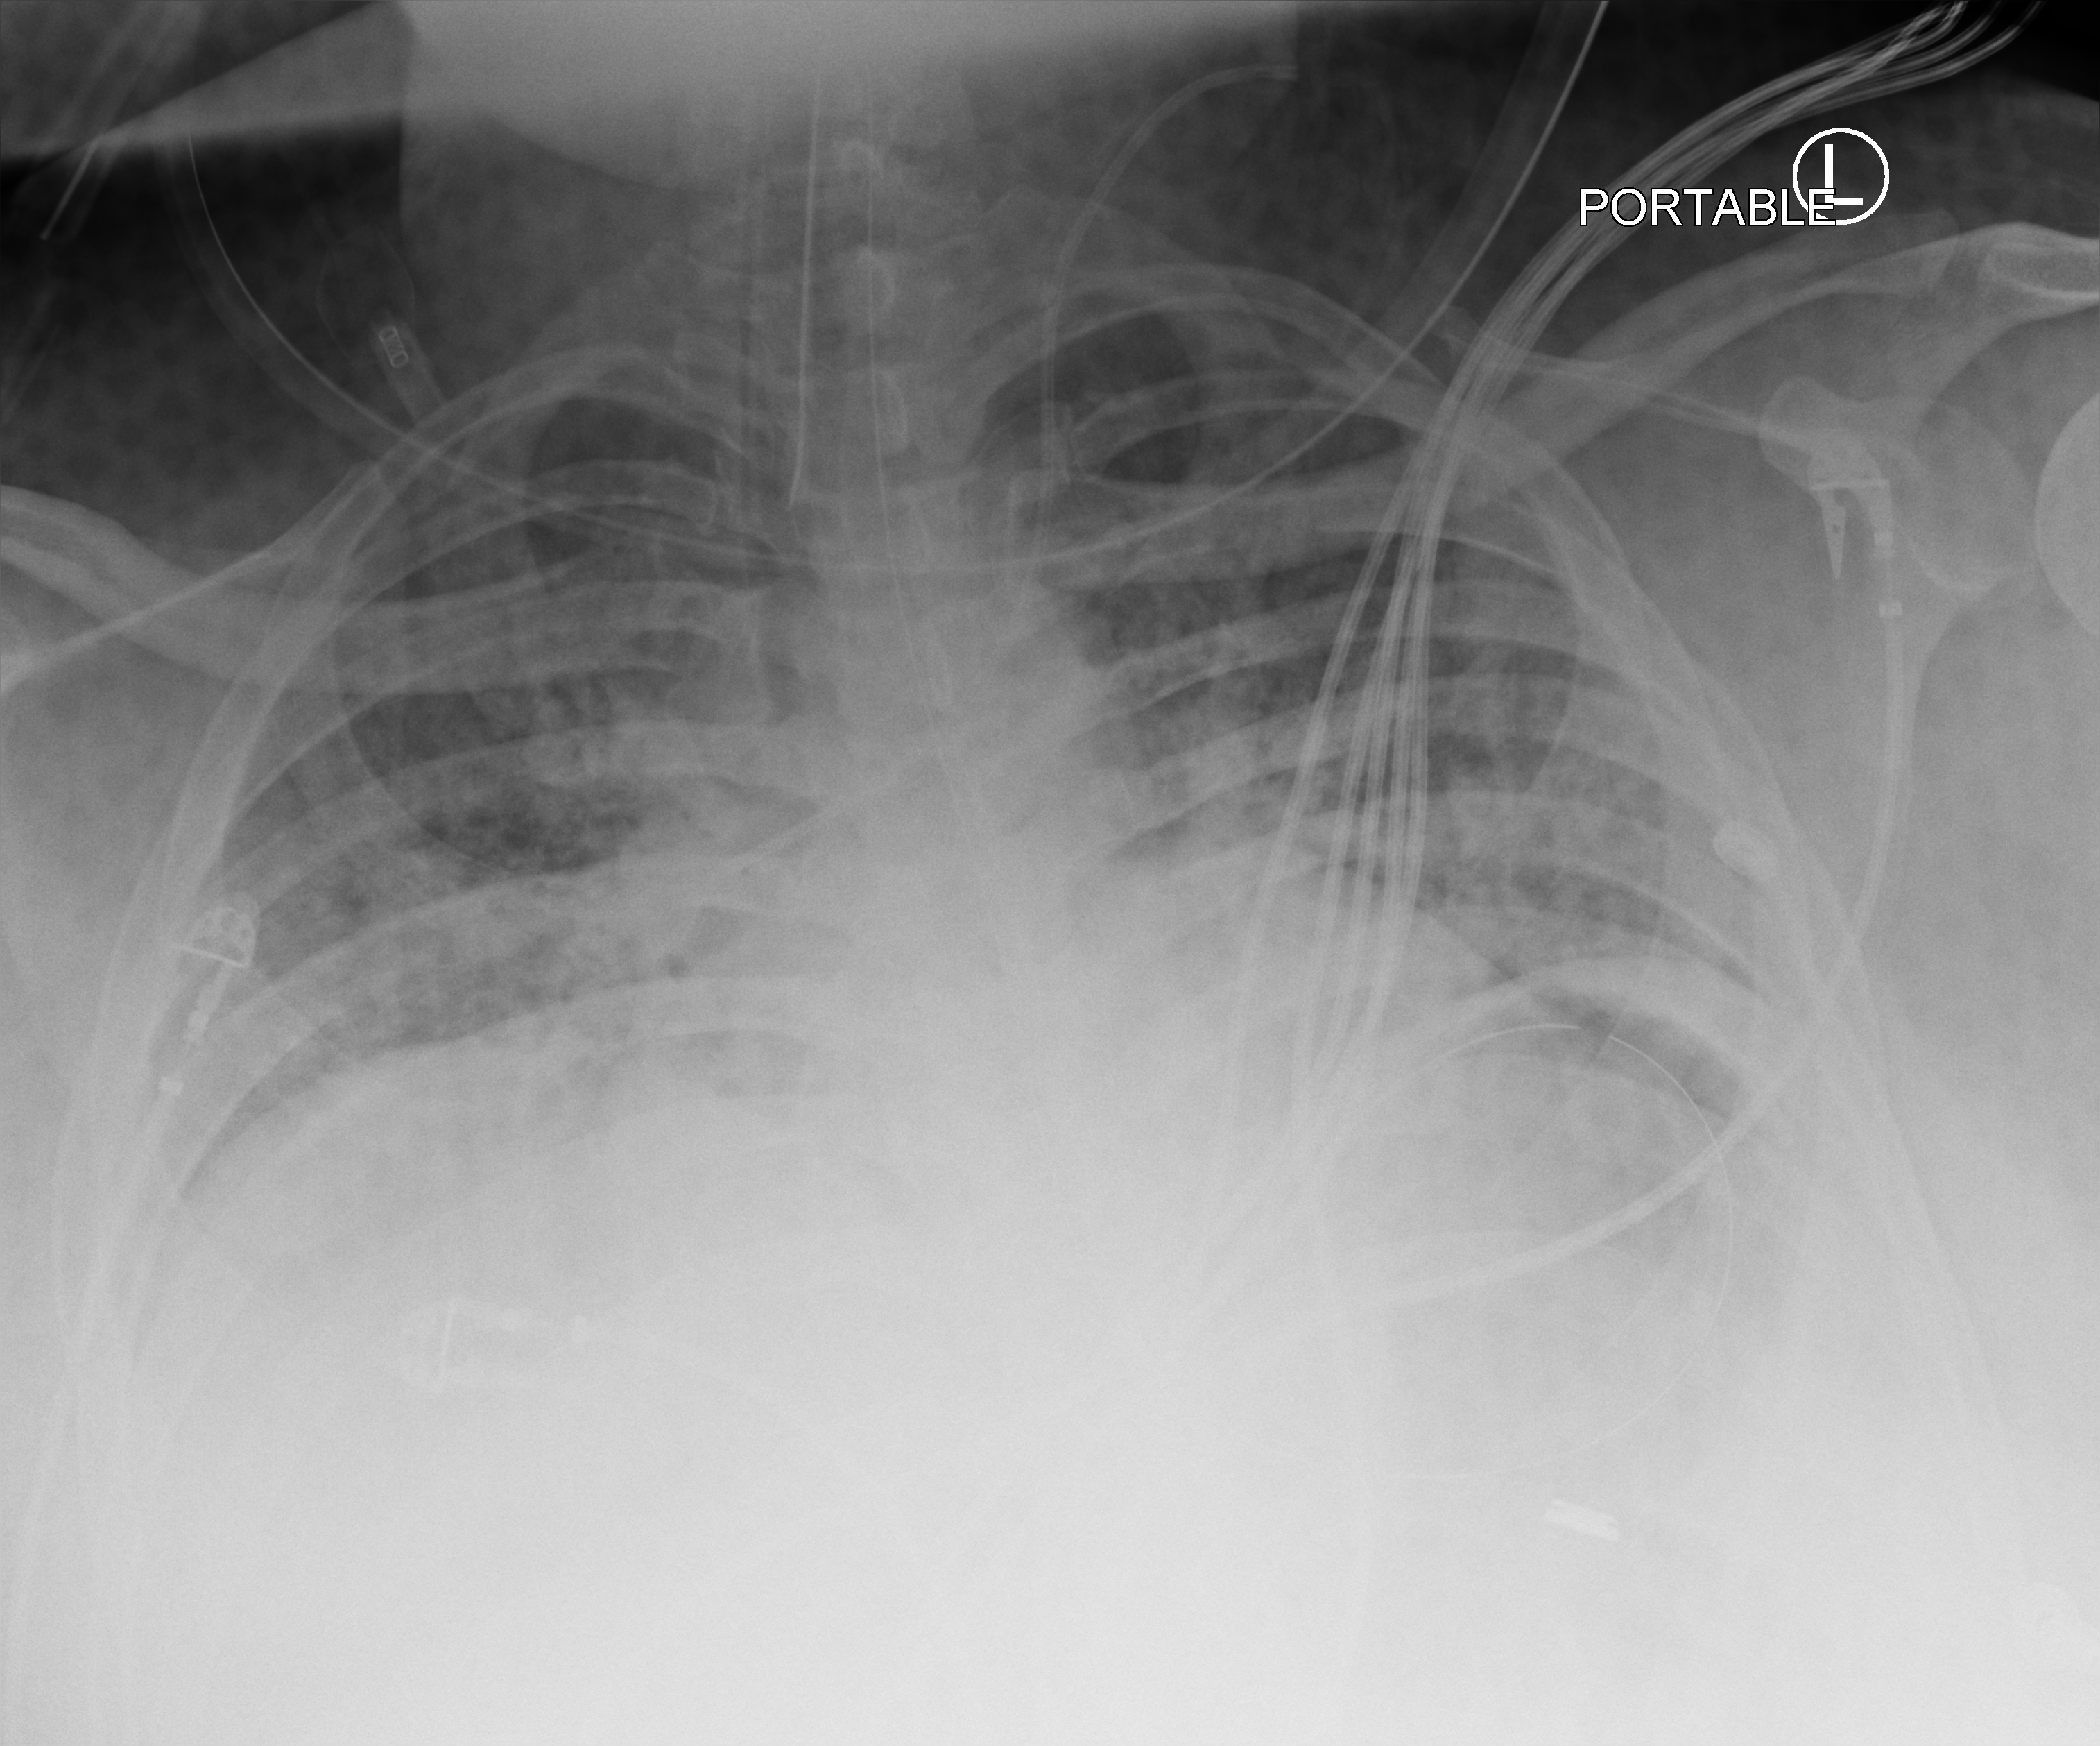
Portable chest radiograph; anteroposterior (AP) projection. Male patient hospitalised with COVID-19, age 18–59 years.
Hospital-stay facts (about this admission, not read from this image; timing relative to this image not recorded): mechanically ventilated during this hospital stay: yes.